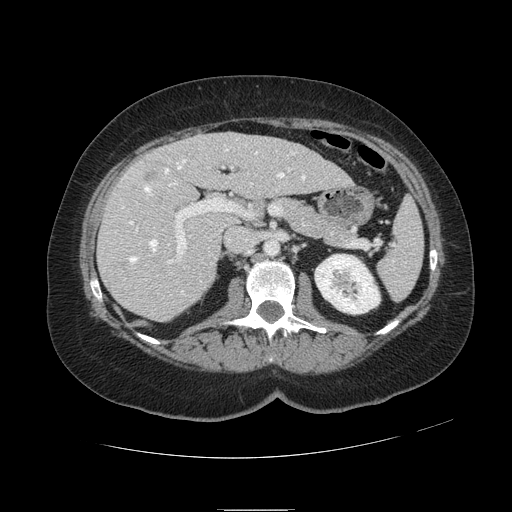
Contrast-enhanced abdominal CT, one axial slice. Position 55 of 121 along the scan axis. 120 kVp. Soft-tissue window (W 400 / L 40 HU). 2.5 mm slice thickness. 512 × 512 image matrix, field of view 400 × 400 mm. Female patient, age 52 years. From the clinical record (not read from this slice): diagnosis: colorectal cancer liver metastases, imaged before liver resection; multiple liver metastases: yes; largest metastasis: 6.3 cm; disease in both lobes: no.
Annotated regions visible in this slice (outlined manually by an expert reader):
- hepatic veins: bounding box [x1, y1, x2, y2] px = [123, 148, 305, 293]
- liver: [99, 133, 349, 321]
- planned liver remnant (the part of the liver to remain after resection): [169, 134, 349, 198]
- portal vein (with intrahepatic branches): [130, 168, 291, 263]
- liver metastasis: [143, 170, 154, 180]